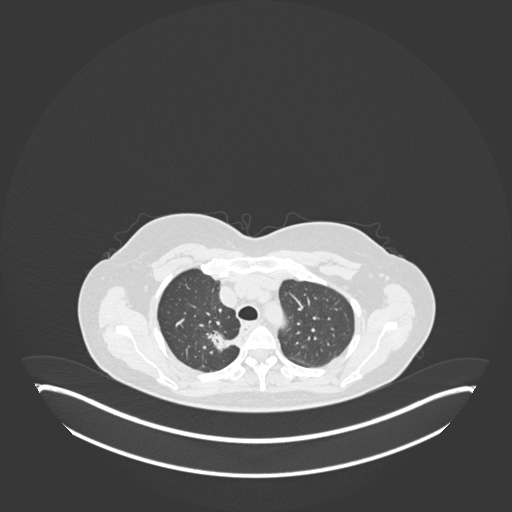
Chest CT, one axial slice. Position 138 of 181 along the scan axis. Reconstruction kernel B30f. 120 kVp. Lung window (W 1500 / L -600 HU). 1 mm slice thickness. 512 × 512 image matrix, field of view 500 × 500 mm. Patient: female, 65 years. From the clinical record (not read from this slice): clinical TNM (as recorded): T1b N0 M0; histopathological grade: G2.
Structures marked on this image (rectangle marked by the reading radiologist):
- lung tumour (recorded histology: adenocarcinoma): bounding box (x1, y1, x2, y2) in pixels: (205, 323, 240, 353)